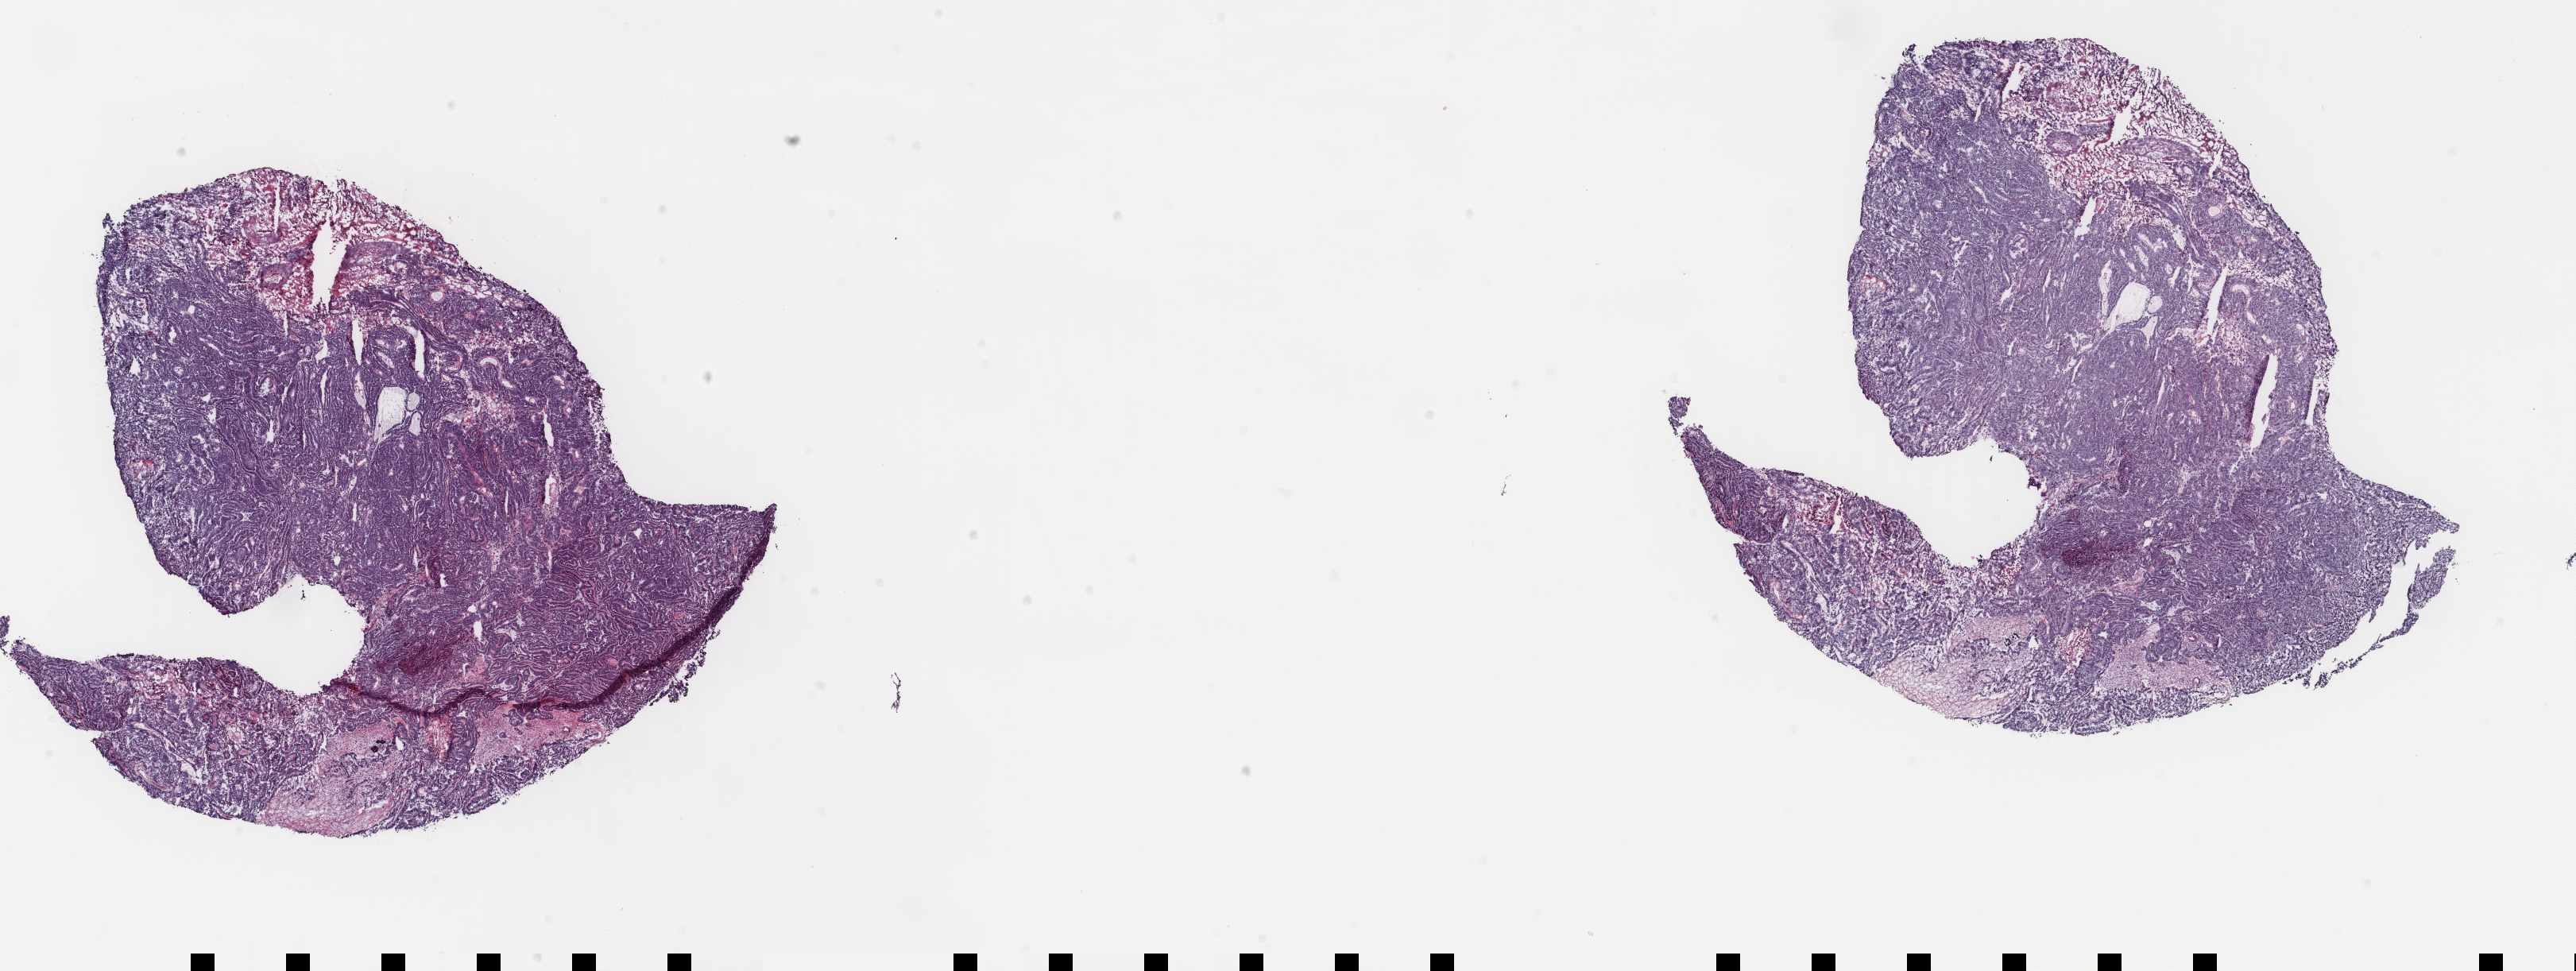
Digitized H&E tissue section (whole slide), whole scanned area (about 25.7 x 9.7 mm, from a 40x scan) shown as a low-resolution overview, frozen section from the top of the tissue portion, ovary, primary tumour sample. Patient: female, age at initial diagnosis 48 years. Histologic grade: G3 (poorly differentiated). Composition of this section per pathologist review: tumour cells 95%, tumour nuclei 80%, normal cells 0%, stromal cells 0%, necrosis 5%. Inflammatory infiltration, as recorded: lymphocyte infiltration 2%, monocyte infiltration 1%, neutrophil infiltration 0%.
Diagnosis: Papillary serous cystadenocarcinoma. FIGO stage: IIIB.